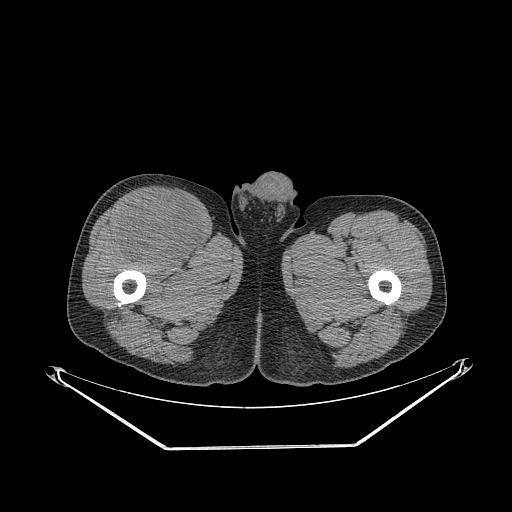
CT of an extremity soft-tissue mass (from a PET/CT study), one axial slice. Slice 291 of 311 in the series (ordered by position). Reconstruction kernel STANDARD. 140 kVp. Soft-tissue window (W 400 / L 40 HU). 512 × 512 image matrix, field of view 500 × 500 mm. Male patient. Case-level facts recorded for this patient, not image findings: histological type: pleiomorphic leiomyosarcoma; grade: intermediate; site of the primary tumour: right thigh.
Structures marked on this image (expert contour drawn on MRI and transferred to this co-registered scan by the dataset authors):
- gross tumour volume including surrounding oedema: bounding box [x1, y1, x2, y2] px = [116, 192, 206, 266]
- gross tumour volume (mass): [116, 192, 206, 266]